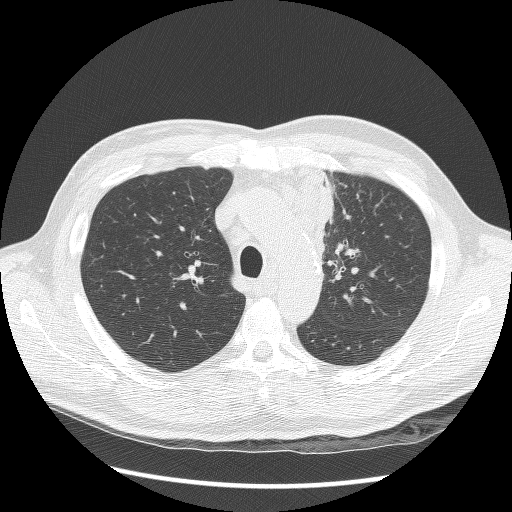
Axial slice from a low-dose chest CT screening exam. Second screening round (one year after baseline). Lung window (W 1500 / L -600 HU). Lung (sharp) reconstruction kernel (BONE). 120 kVp. 512 × 512 image matrix. Male participant, aged 64 years at enrolment. Former smoker at enrolment.
• Expert-annotated lung lesion, bounding box [x1, y1, x2, y2] px = [295, 176, 363, 293].
• Screening reader's record for this exam: no non-calcified nodule ≥4 mm recorded.
• Lung cancer was diagnosed 24 days after this screen: small cell carcinoma, NOS, left upper lobe, stage IV (AJCC 6th edition), 100 mm at pathology.